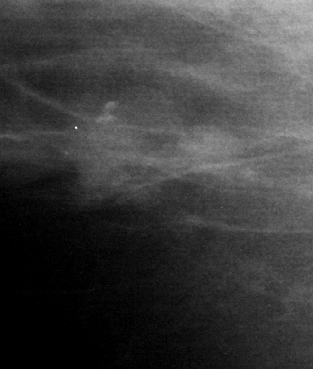
Crop from a digitized film mammogram around one marked abnormality, right breast, MLO view.
- Calcifications, morphology amorphous, distribution clustered; BI-RADS assessment category 4; pathology (as recorded): benign.